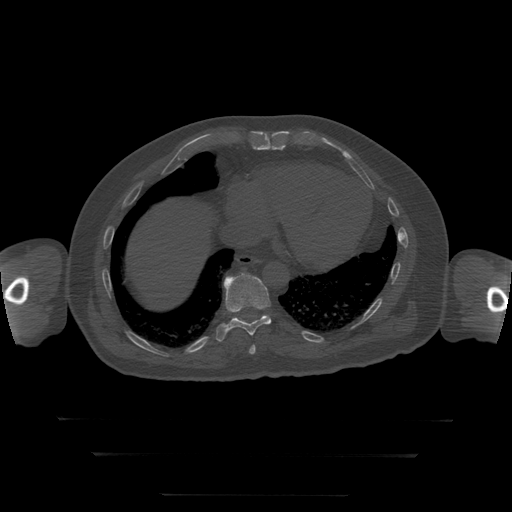
CT including the spine, one axial slice; position 122 of 397 along the scan axis; reconstruction kernel STANDARD; bone window (W 1800 / L 400 HU); 1.25 mm slice thickness; 512 × 512 image matrix, field of view 510 × 510 mm. Patient age 73 years. From the clinical record (not read from this slice): primary cancer: prostate.
Annotated regions visible in this slice (semi-automatically segmented with operator editing):
- T10 vertebra: bounding box (x1, y1, x2, y2) in pixels: (216, 273, 272, 342)
- T9 vertebra: (249, 346, 256, 355)